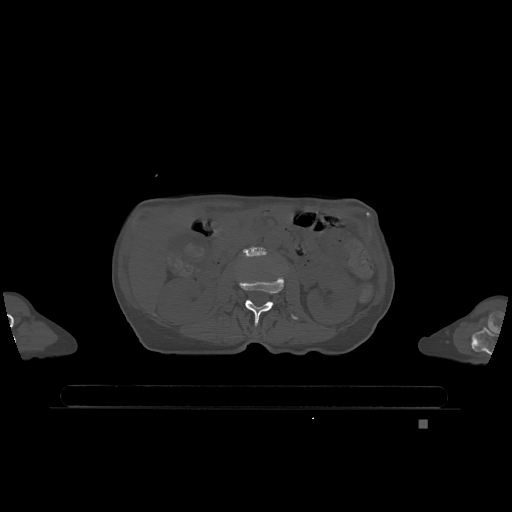
CT including the spine, one axial slice; slice 405 of 1317 in the series (ordered by position); bone window (W 1800 / L 400 HU); 512 × 512 image matrix. Patient: female, 74 years. From the clinical record (not read from this slice): primary cancer: lung.
Structures marked on this image (semi-automatically segmented with operator editing):
- L2 vertebra: bounding box <239,274,298,326> (left, top, right, bottom; pixels)
- L3 vertebra: <243,246,266,256>